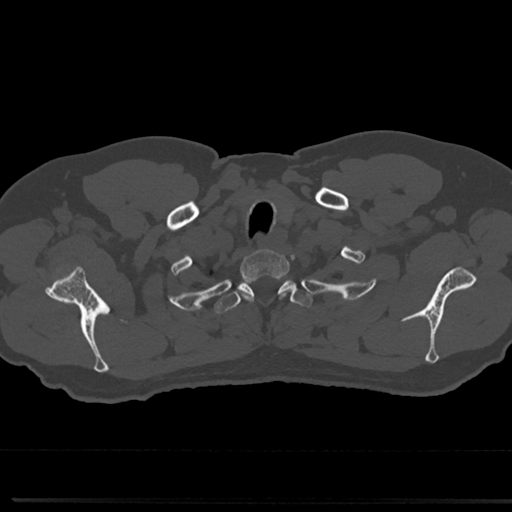
CT including the spine, one axial slice; slice 652 of 817 in the series (ordered by position); reconstruction kernel Br40s/3; 120 kVp; bone window (W 1800 / L 400 HU); 0.5 mm slice thickness; 512 × 512 image matrix, field of view 355 × 355 mm. Male patient, age 61 years. Case-level facts recorded for this patient, not image findings: primary cancer: prostate.
Outlined on this slice (semi-automatically segmented with operator editing):
- T1 vertebra: bounding box [x1, y1, x2, y2] px = [242, 251, 287, 275]
- T2 vertebra: [222, 274, 306, 319]